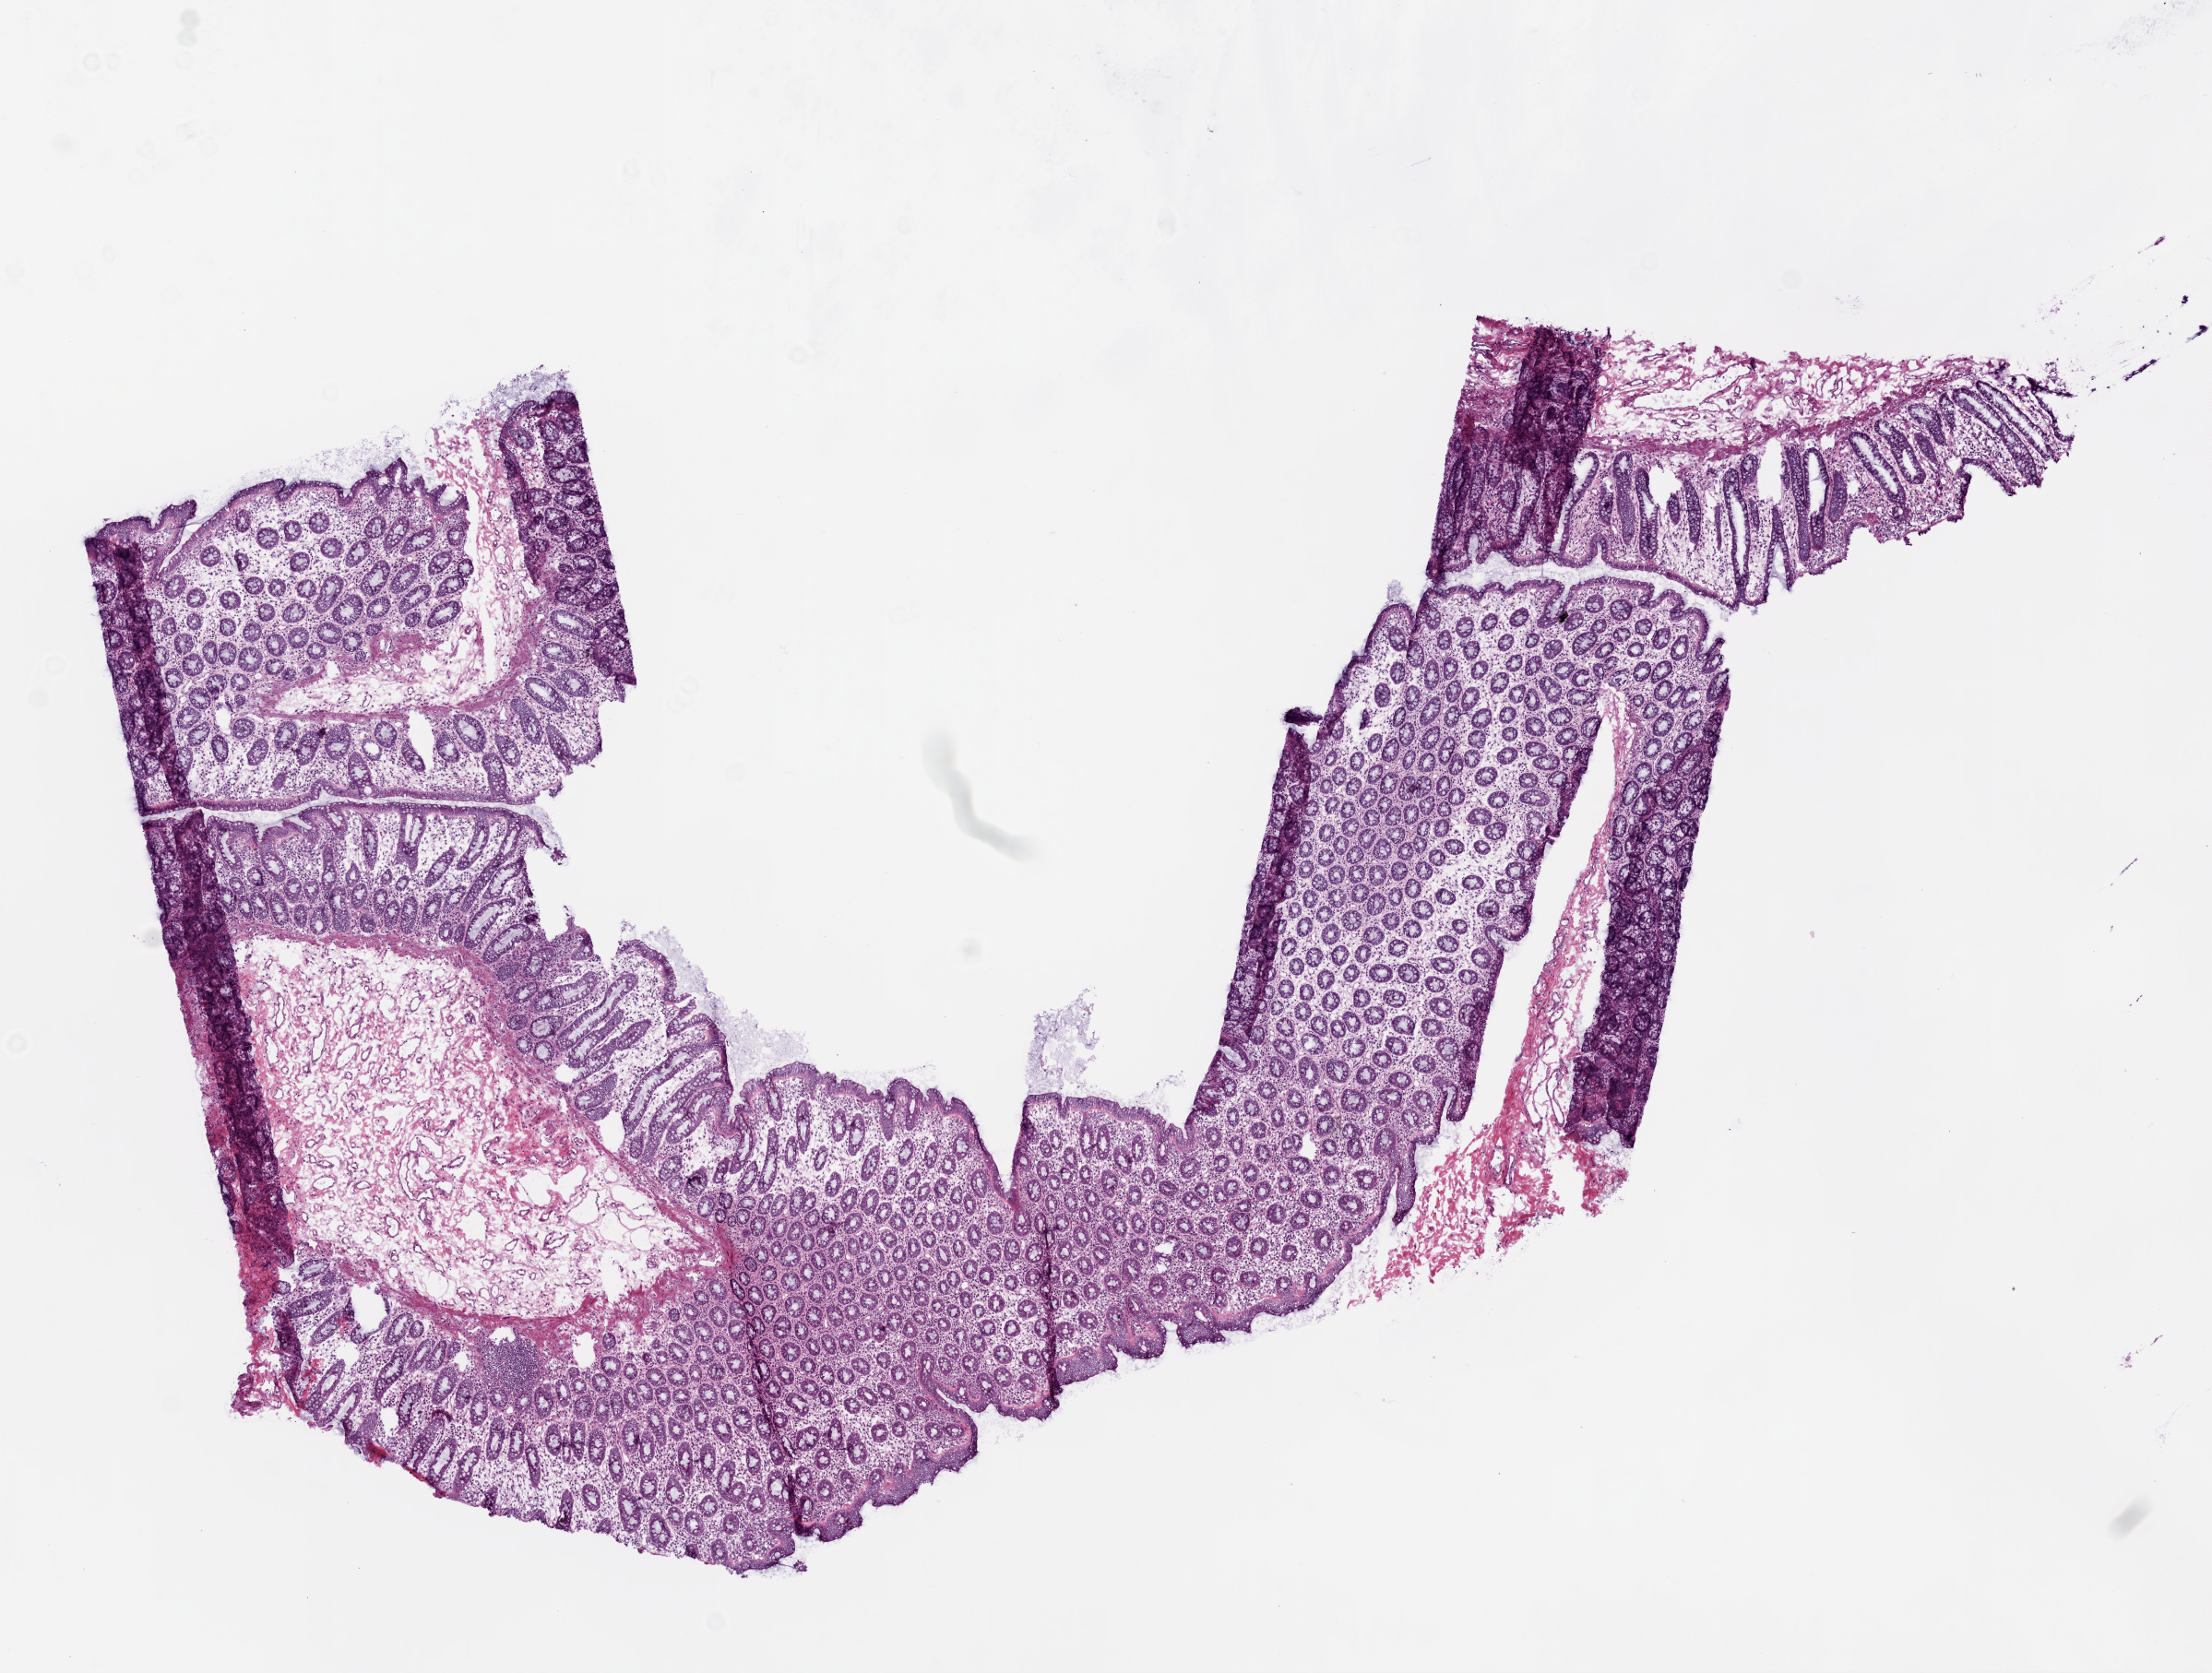
Digitized H&E-stained tissue section (whole slide) — low-resolution overview of the scanned area, about 9.7 x 7.3 mm; frozen section; sample: solid tissue normal (non-tumour tissue), rectum. Female, age 73 years at initial diagnosis.
This section: solid tissue normal sample (biorepository sample class). Patient diagnosis: Adenocarcinoma, NOS (rectosigmoid junction).